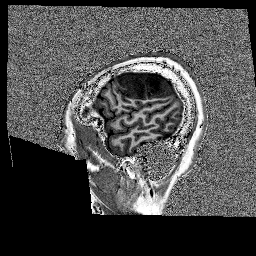
Brain MRI from a brain-tumour surgery series, one sagittal slice. Position 33 of 176 along the scan axis. 1 mm slice thickness. 256 × 256 image matrix, field of view 256 × 256 mm. Case-level facts recorded for this patient, not image findings: histopathology: Glioblastoma; WHO grade: 4; IDH mutation: no.
Outlined on this slice (expert manual segmentation):
- tumour: bounding box (x1, y1, x2, y2) in pixels: (118, 72, 175, 99)